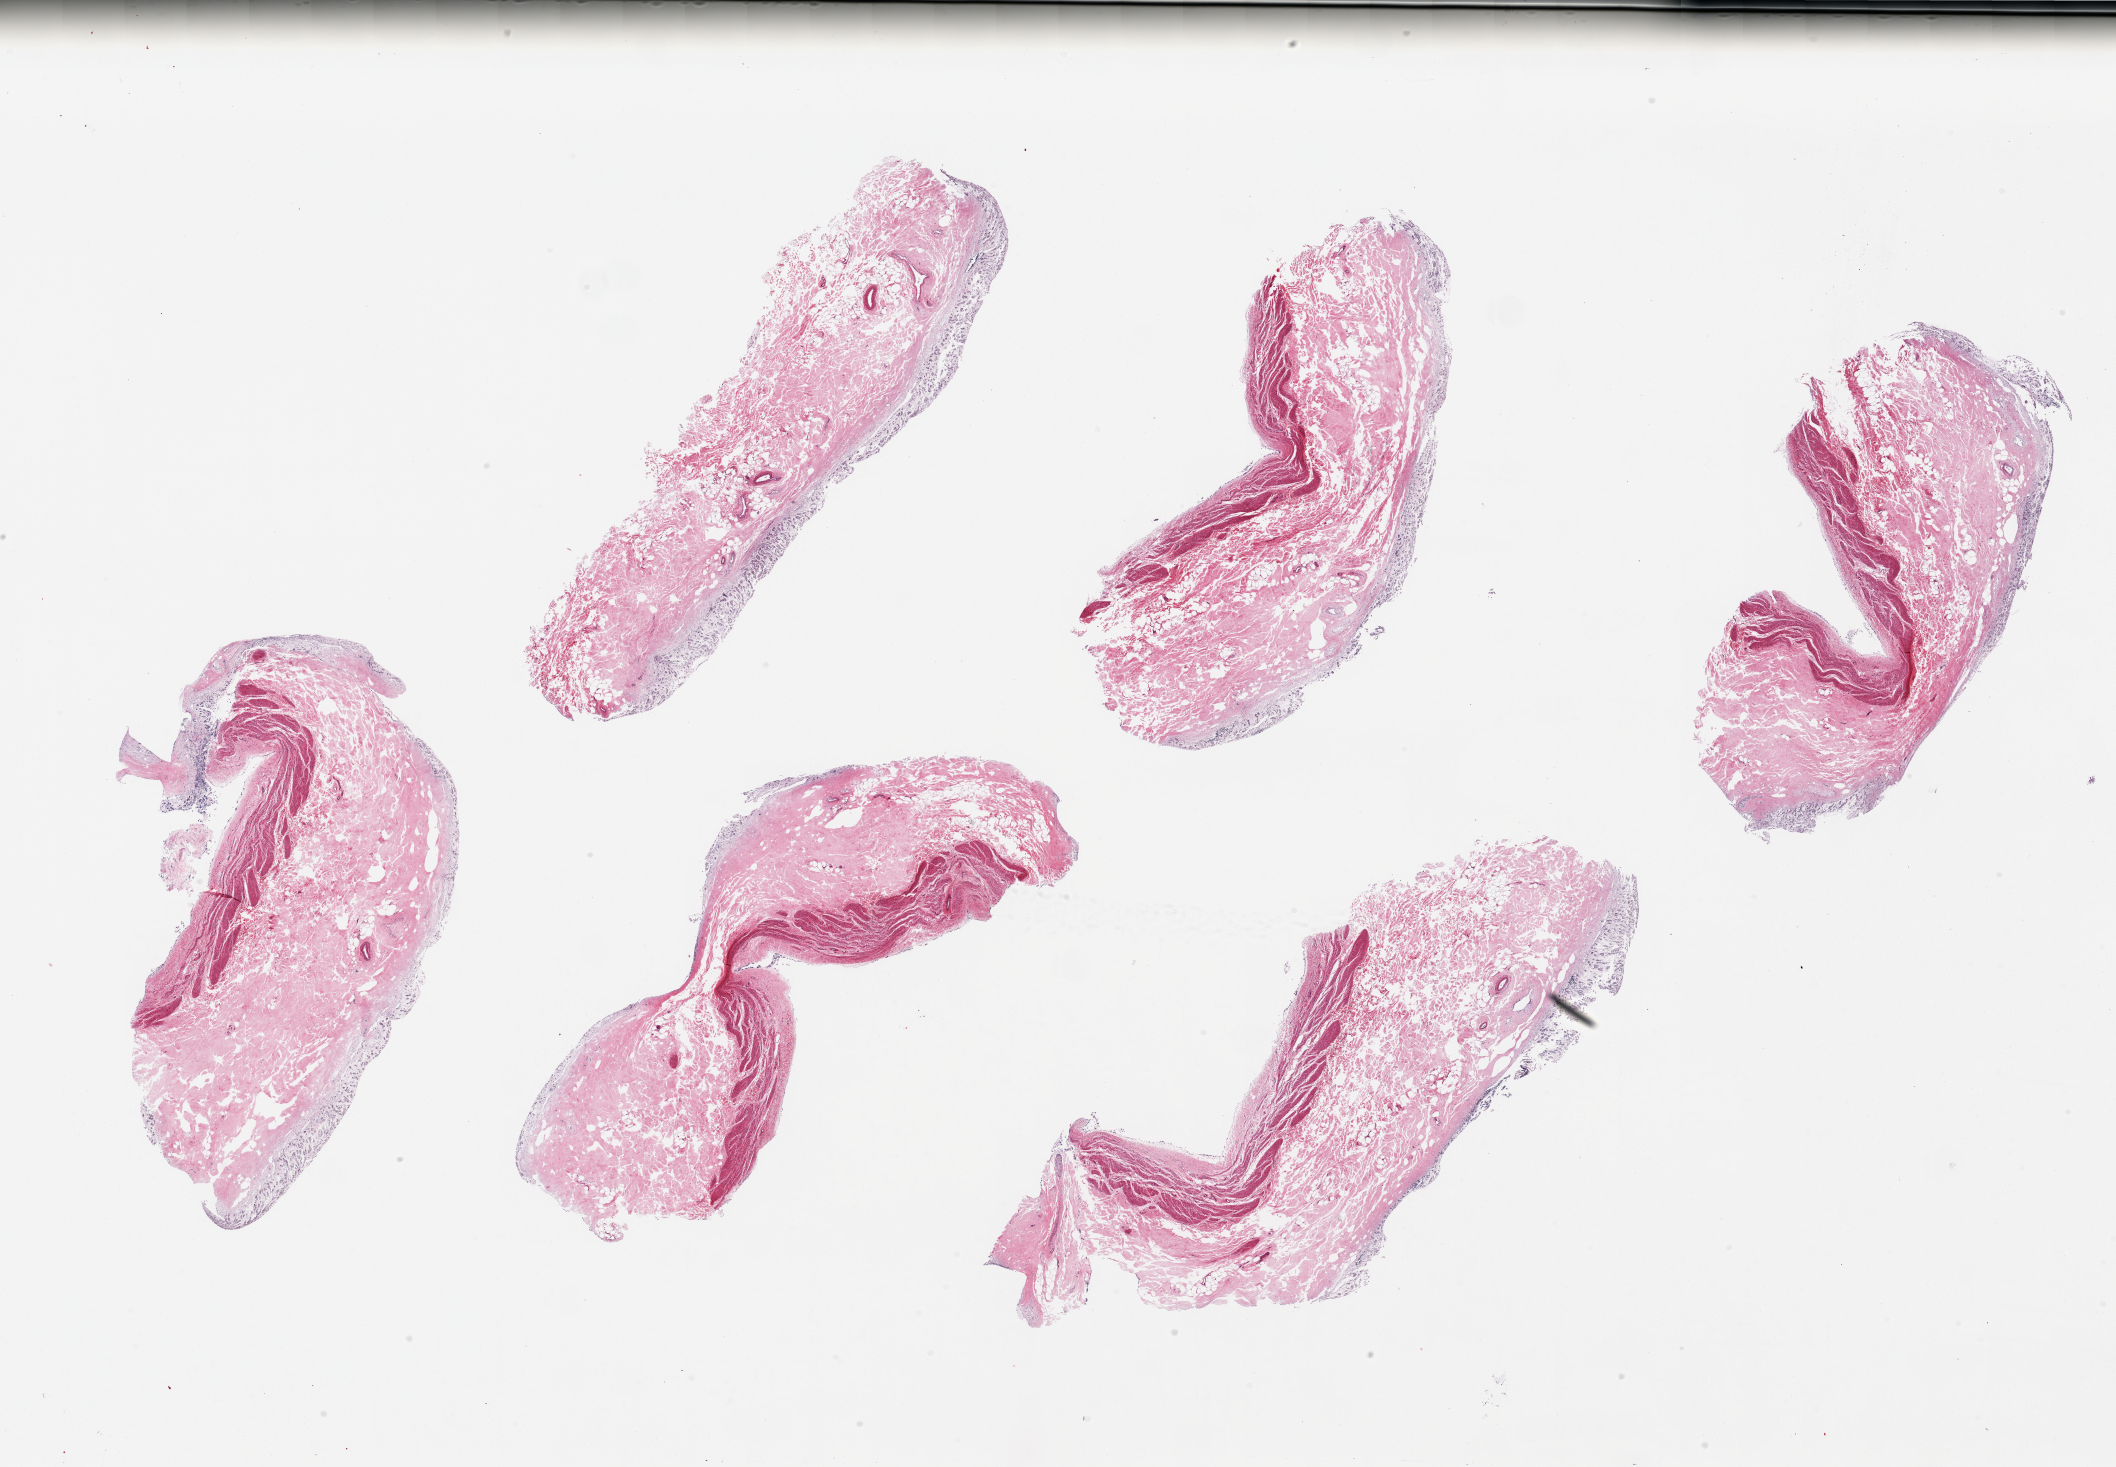
Digitized haematoxylin and eosin-stained section — shown as a low-resolution overview of the whole scanned area (about 33.5 x 23.2 mm, from a 20x scan); PAXgene-fixed paraffin-embedded (PFPE) section; sampled site (target tissue): stomach; tissue donor sample. Donor sex: male.
Review note (as recorded): 6 pieces ~9x3.5mm. Mucosa totally autolyzed, partly sloughed.